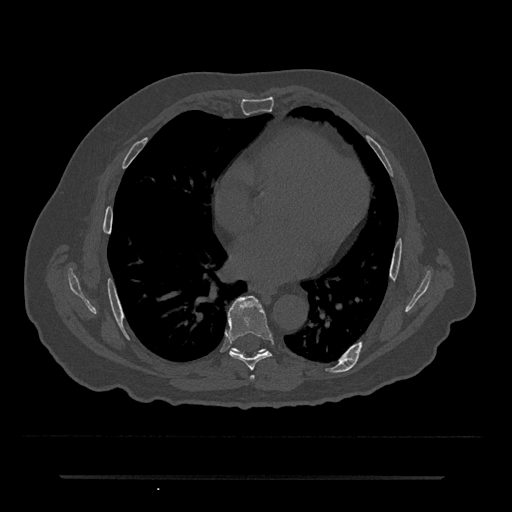
CT including the spine, one axial slice; slice 373 of 797 in the series (ordered by position); 120 kVp; bone window (W 1800 / L 400 HU); 0.5 mm slice thickness; 512 × 512 image matrix, field of view 437 × 437 mm. Male patient, age 69 years. From the clinical record (not read from this slice): primary cancer: prostate.
Structures marked on this image (semi-automatically segmented with operator editing):
- T6 vertebra: bounding box [x1, y1, x2, y2] px = [250, 375, 255, 380]
- T7 vertebra: [227, 296, 272, 370]
- T8 vertebra: [232, 348, 264, 354]